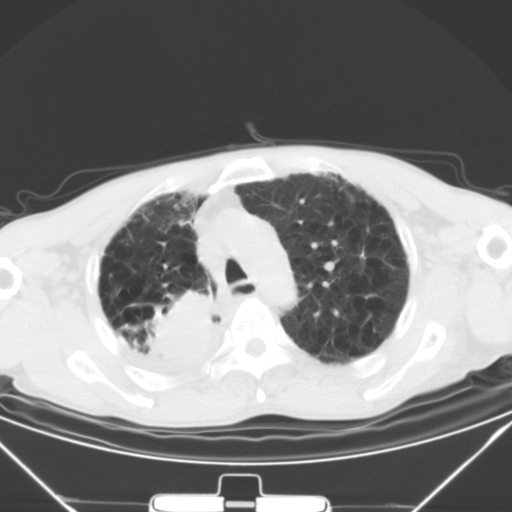
Chest CT, one axial slice. Slice 37 of 50 in the series (ordered by position). 120 kVp. Lung window (W 1500 / L -600 HU). 5 mm slice thickness. 512 × 512 image matrix, field of view 373 × 373 mm. Patient: male, 65 years. Case-level facts recorded for this patient, not image findings: clinical TNM (as recorded): T3 N1 M1a.
Structures marked on this image (bounding box drawn by a radiologist):
- lung tumour (recorded histology: squamous cell carcinoma): bounding box [x1, y1, x2, y2] px = [131, 284, 234, 378]